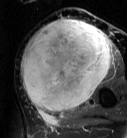
MRI of an extremity soft-tissue mass, one axial slice; slice 36 of 87 in the series (ordered by position); T2-weighted fat-saturated; MR volume resampled by the dataset authors to the PET/CT grid (not the native acquisition matrix); 127 × 138 image matrix, field of view 124 × 135 mm. Female patient. Case-level facts recorded for this patient, not image findings: histological type: pleiomorphic leiomyosarcoma; grade: high; site of the primary tumour: left biceps.
Structures marked on this image (expert contour drawn on MRI and transferred to this co-registered scan by the dataset authors):
- gross tumour volume including surrounding oedema: bounding box <20,18,112,113> (left, top, right, bottom; pixels)
- gross tumour volume (mass): <20,20,110,113>